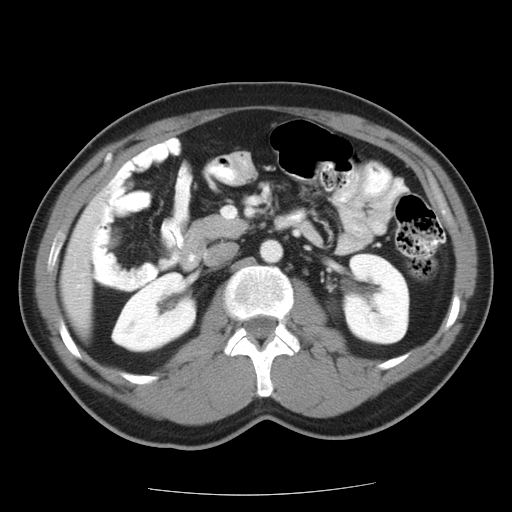
Contrast-enhanced abdominal CT, one axial slice. Slice 4 of 22 in the series (ordered by position). Reconstruction kernel STANDARD. 120 kVp. Intravenous contrast given. Soft-tissue window (W 400 / L 40 HU). 512 × 512 image matrix. Male patient, age 41 years. Case-level facts recorded for this patient, not image findings: diagnosis: colorectal cancer liver metastases, imaged before liver resection; multiple liver metastases: no; largest metastasis: 2.7 cm.
Outlined on this slice (manually delineated by an expert):
- liver: bounding box <63,214,93,320> (left, top, right, bottom; pixels)
- planned liver remnant (the part of the liver to remain after resection): <63,214,94,319>